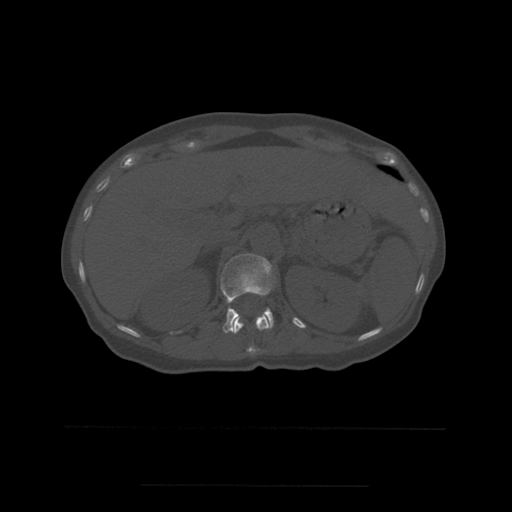
CT including the spine, one axial slice. Position 246 of 544 along the scan axis. Bone window (W 1800 / L 400 HU). 1.25 mm slice thickness. 512 × 512 image matrix, field of view 350 × 350 mm. Patient age 58 years. From the clinical record (not read from this slice): primary cancer: lung.
Outlined on this slice (semi-automatically segmented with operator editing):
- L1 vertebra: bounding box <221,254,274,333> (left, top, right, bottom; pixels)
- T12 vertebra: <233,315,270,354>